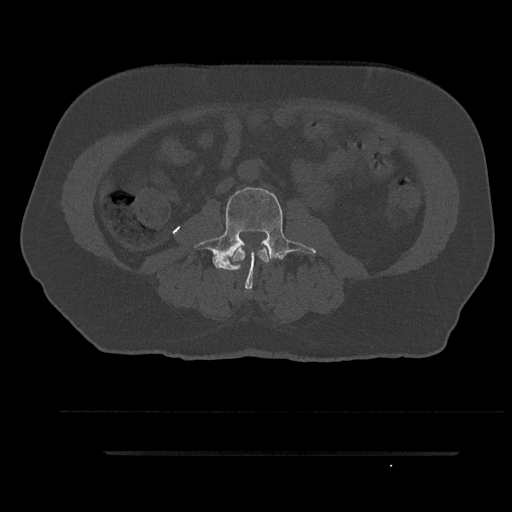
CT including the spine, one axial slice. Position 52 of 797 along the scan axis. Reconstruction kernel Br40s/3. 120 kVp. Bone window (W 1800 / L 400 HU). 512 × 512 image matrix, field of view 432 × 432 mm. Male patient, age 63 years. Case-level facts recorded for this patient, not image findings: primary cancer: renal.
Outlined on this slice (semi-automatically segmented with operator editing):
- L2 vertebra: box from (x=232, y=248) to (x=269, y=271) px
- L3 vertebra: (x=194, y=185)–(x=316, y=289)